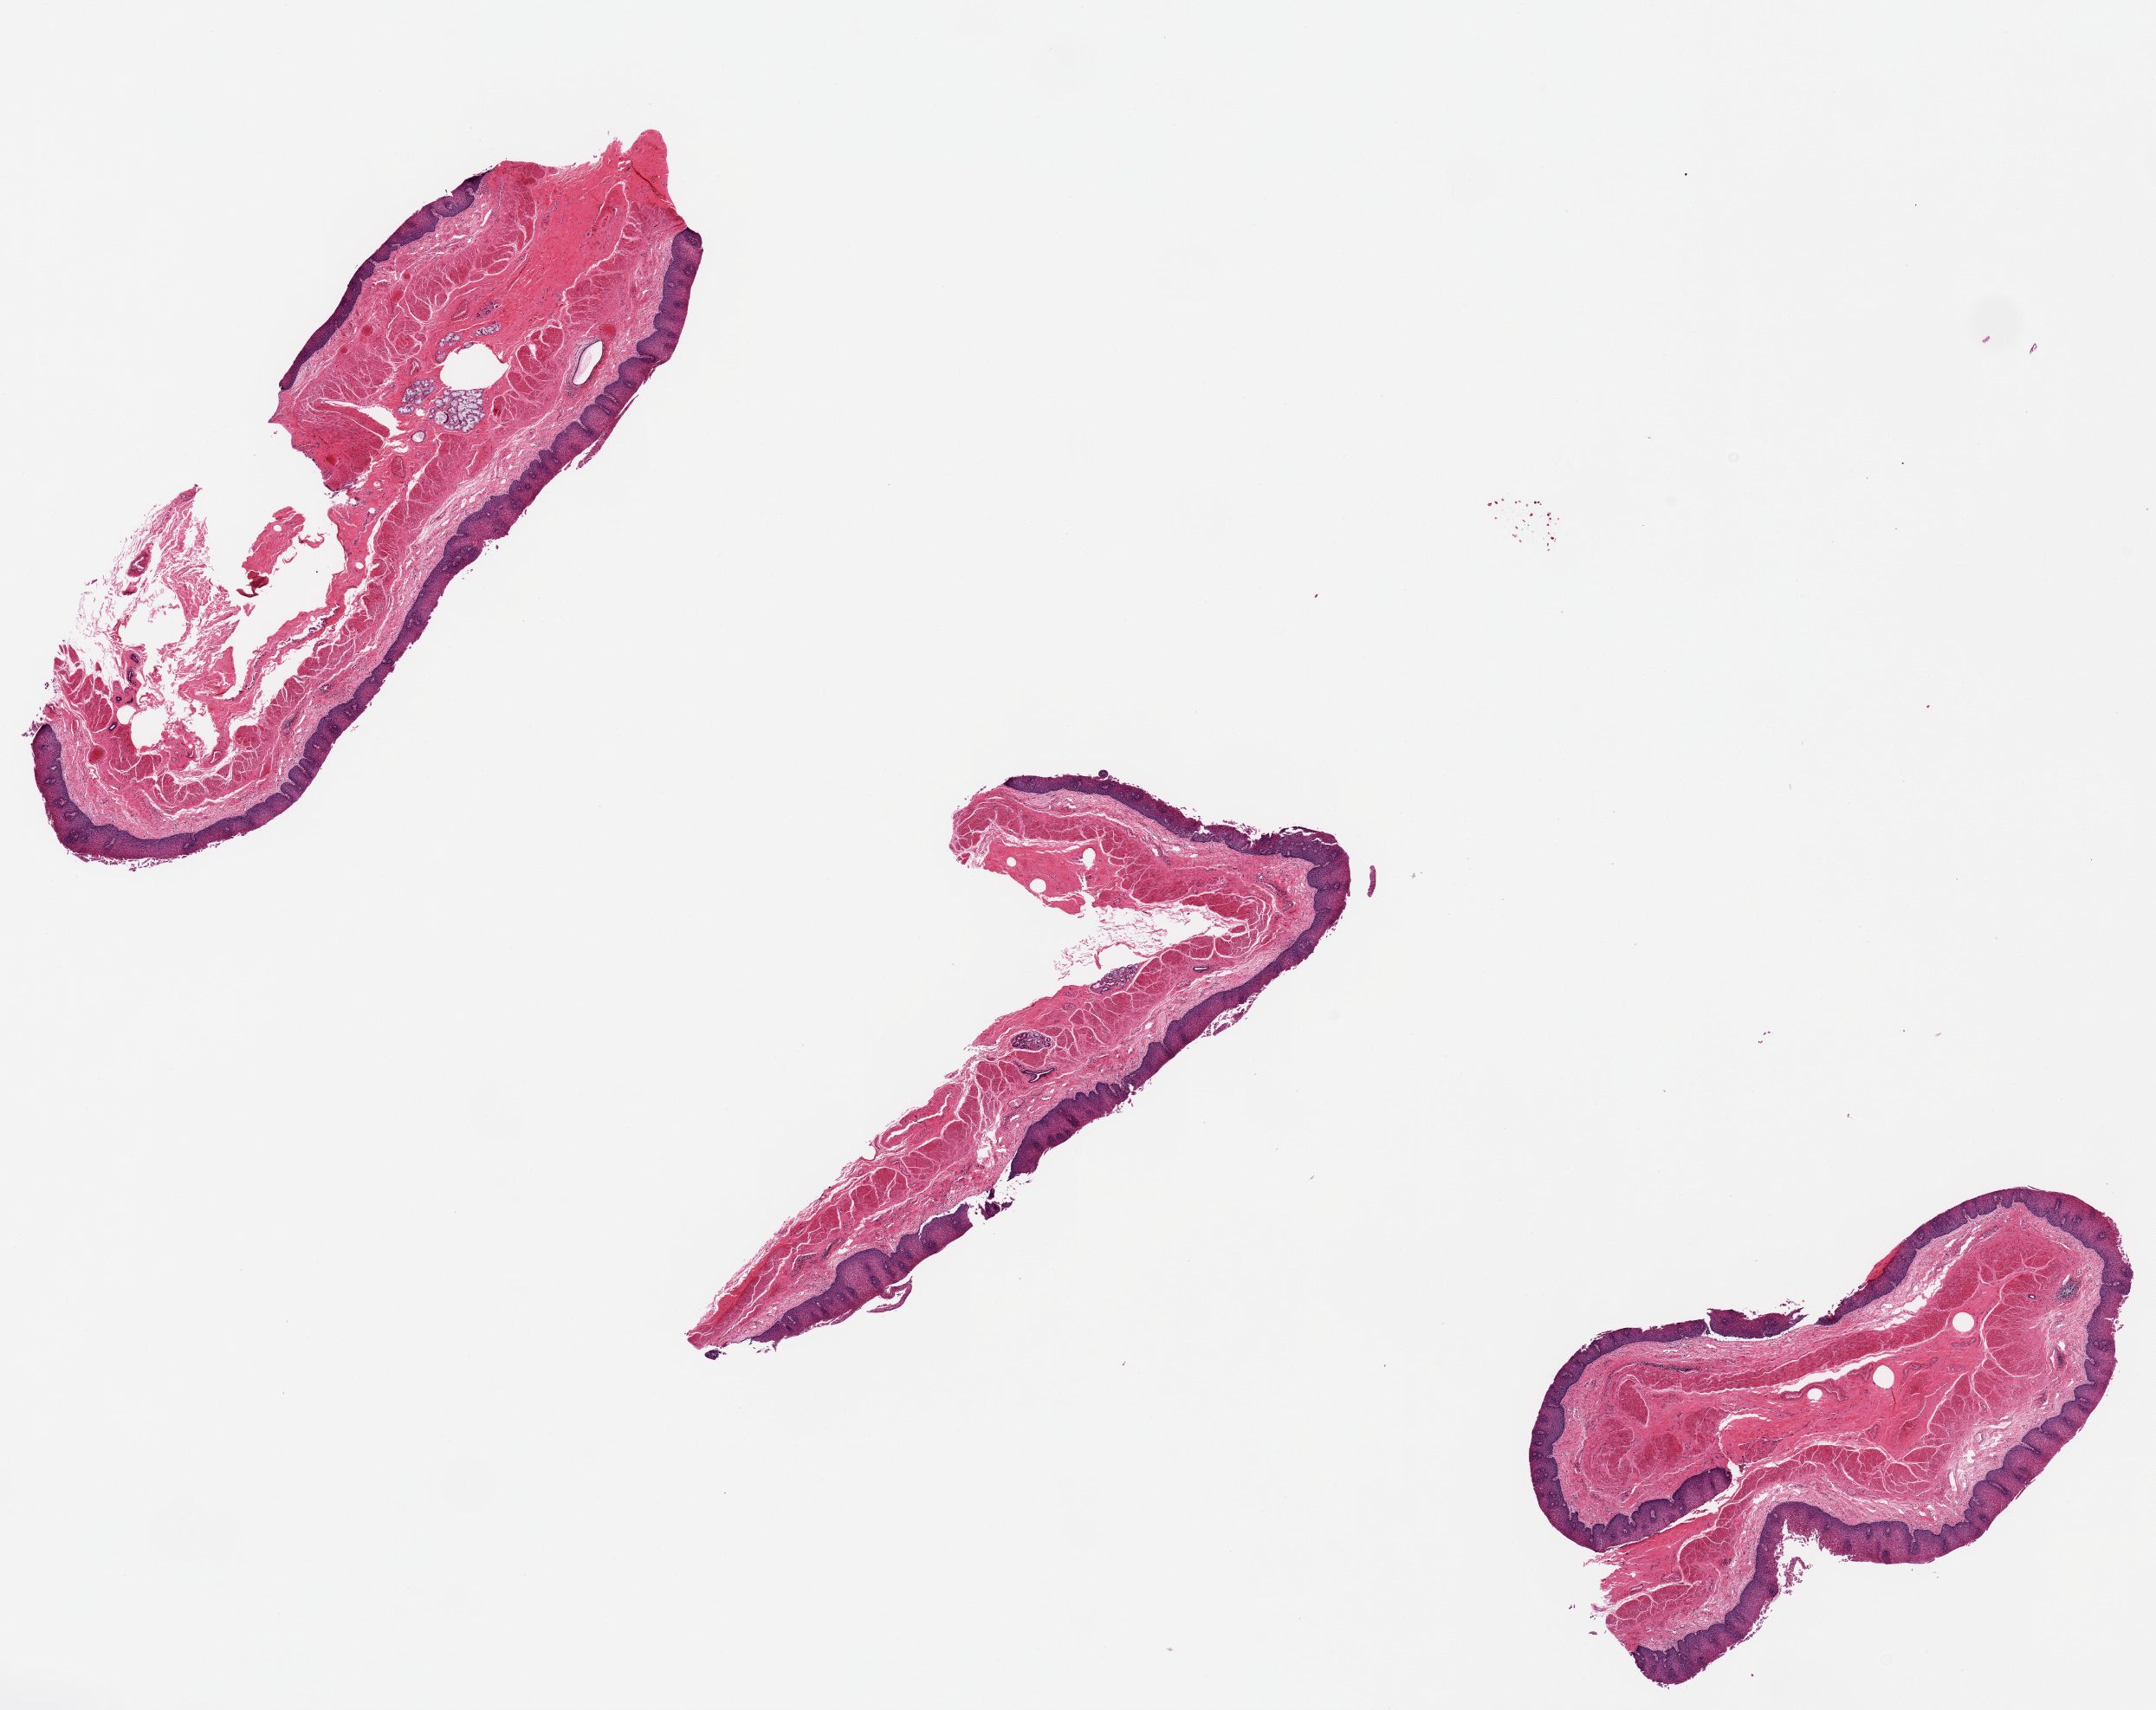
Digitized hematoxylin and eosin (H&E)-stained section, brightfield — a low-resolution overview of the entire scanned area, about 19.7 x 15.6 mm, PAXgene-fixed, paraffin-embedded tissue, target tissue: esophageal mucous membrane, tissue donor sample. Donor sex: male.
• review note (as recorded): 3 pieces; slight epithelial sloughing